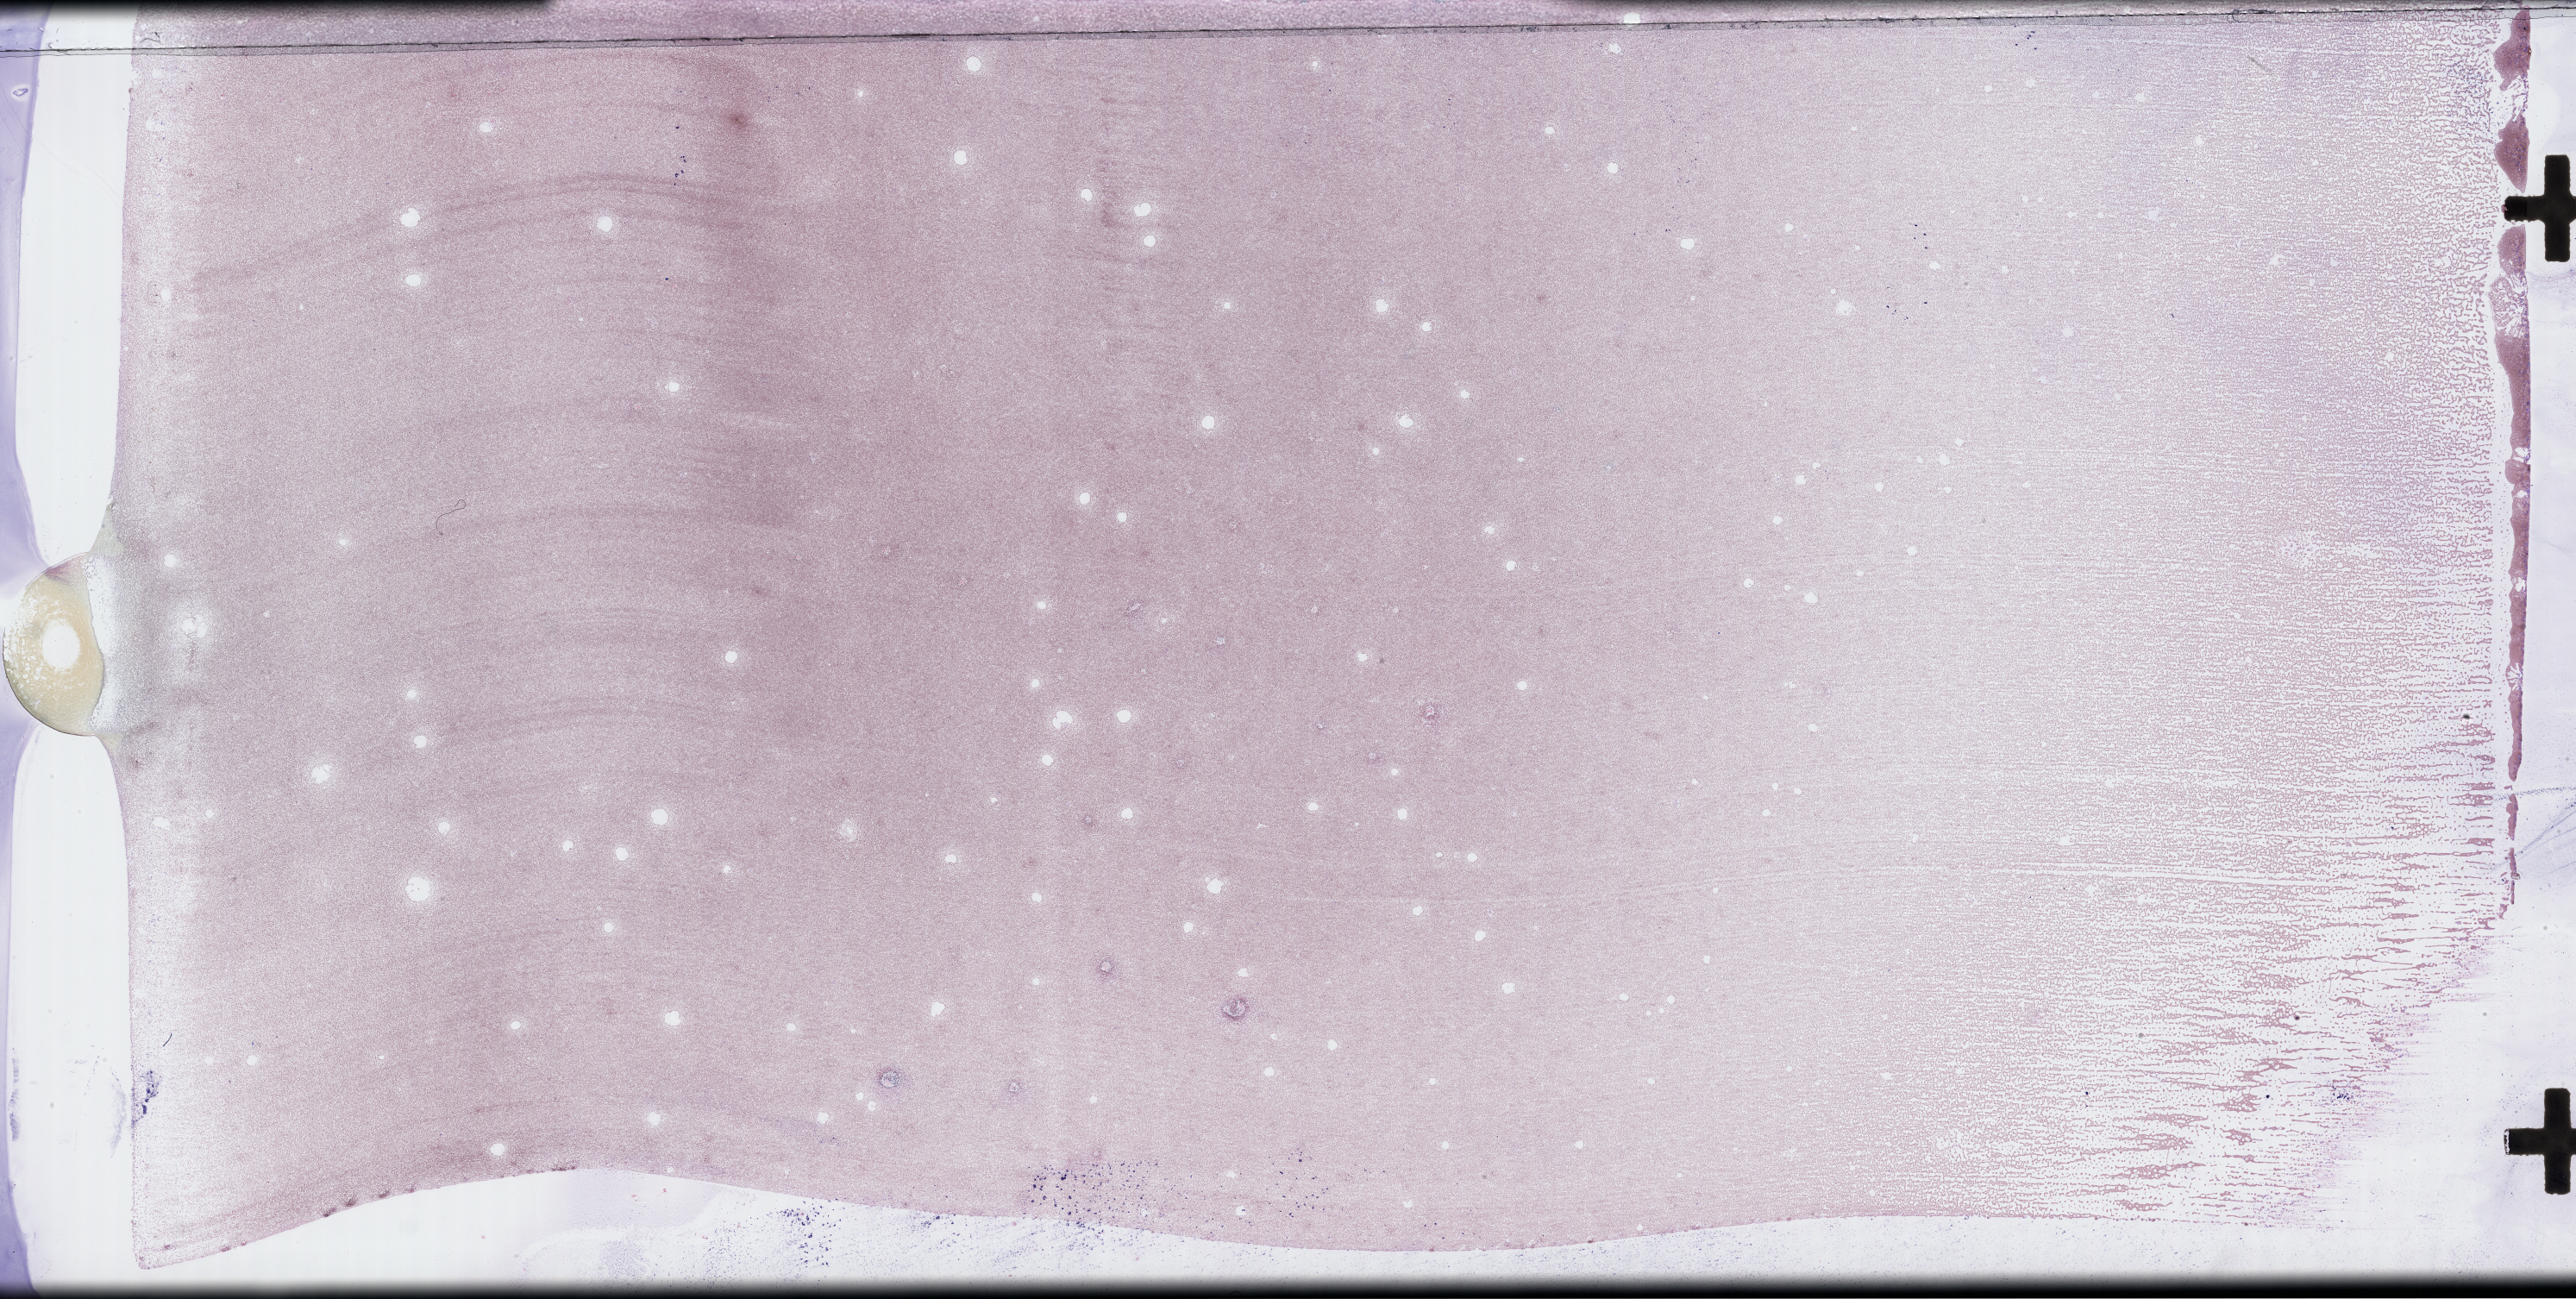
Wright-Giemsa-stained bone marrow smear, whole-slide image, whole scanned area (about 48.2 x 24.3 mm) shown as a low-resolution overview. EDTA-anticoagulated smear. Specimen time point: collected at baseline (before treatment). Patient sex: male.
Patient diagnosis: Plasma Cell Myeloma.